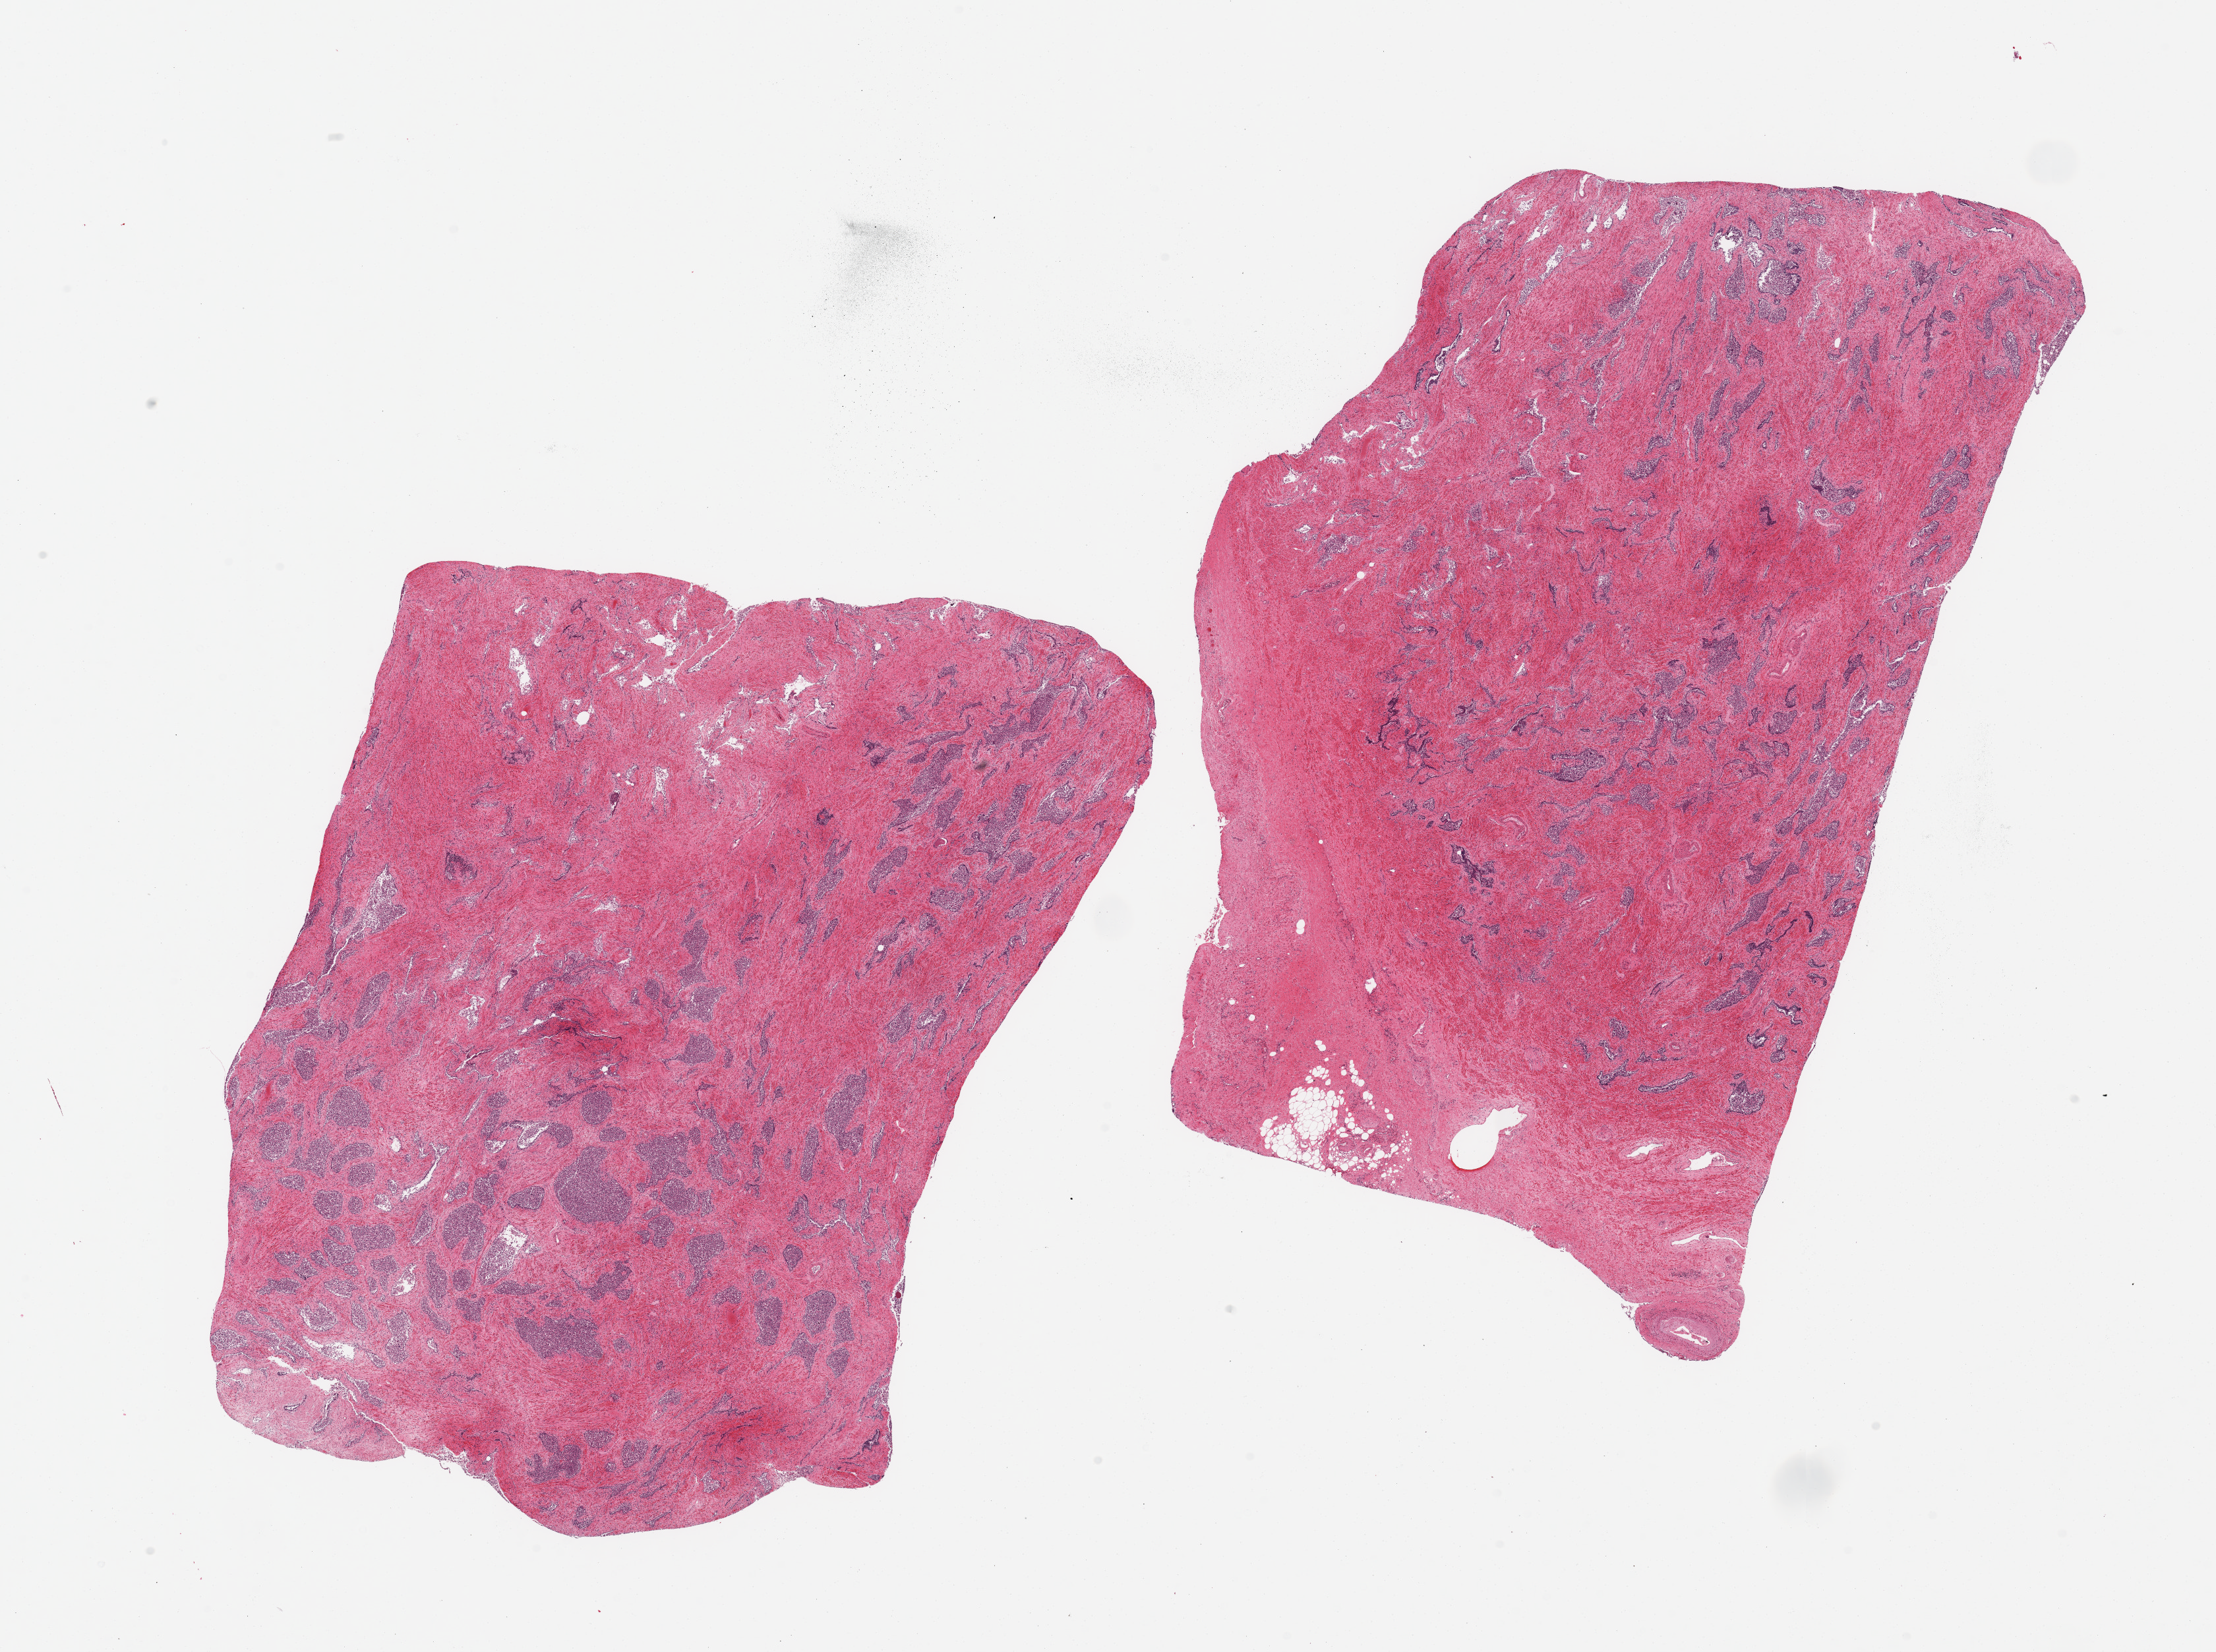
H&E whole-slide image — shown as a low-resolution overview of the whole scanned area (about 26.6 x 19.8 mm), PAXgene-fixed paraffin-embedded (PFPE) section, sampled site (target tissue): prostate, donor tissue sample. Donor sex: male.
* review note (as recorded): 2 pieces, glandular elements completely autolyzed